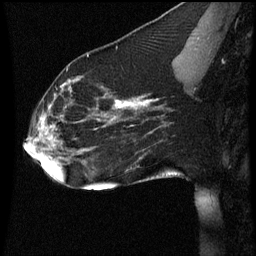
Breast MRI (dynamic contrast-enhanced), one sagittal slice; position 24 of 60 along the scan axis; dynamic contrast-enhanced series, image 2 of 3 at this slice position (ordered by acquisition); 1.5 T; TE 4.2 ms, TR 8.9 ms; 2 mm slice thickness; 256 × 256 image matrix. Patient: female, 35 years. Case-level facts recorded for this patient, not image findings: setting: breast cancer imaged before/during neoadjuvant chemotherapy; receptor status: HER2-positive.
Structures marked on this image (semi-automatically segmented with operator editing):
- analysis volume of interest (the breast-tissue region the enhancement analysis was run in; not a lesion): bounding box <22,66,177,177> (left, top, right, bottom; pixels)
- tumour enhancement mask (voxels above the 70 % enhancement threshold inside the analysis volume of interest): <35,78,158,157>